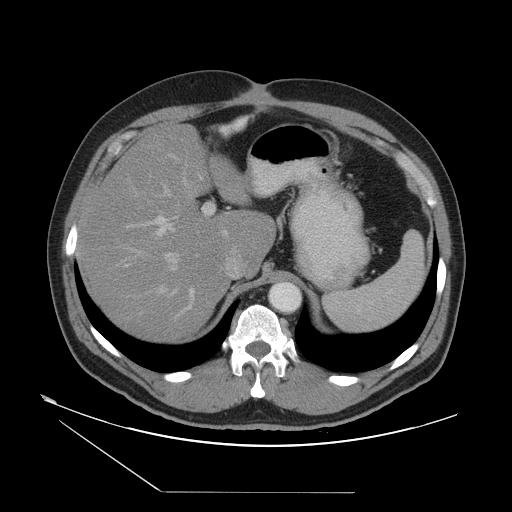
Contrast-enhanced abdominal CT, one axial slice; position 35 of 55 along the scan axis; reconstruction kernel STANDARD; 120 kVp; soft-tissue window (W 400 / L 40 HU); 5 mm slice thickness; 512 × 512 image matrix, field of view 454 × 454 mm. Male patient, age 59 years. From the clinical record (not read from this slice): diagnosis: colorectal cancer liver metastases, imaged before liver resection; multiple liver metastases: yes; largest metastasis: 0.3 cm; disease in both lobes: yes.
Outlined on this slice (expert manual segmentation):
- hepatic veins: box from (x=128, y=179) to (x=197, y=320) px
- liver: (x=79, y=123)–(x=275, y=340)
- planned liver remnant (the part of the liver to remain after resection): (x=80, y=146)–(x=274, y=340)
- portal vein (with intrahepatic branches): (x=124, y=155)–(x=227, y=319)